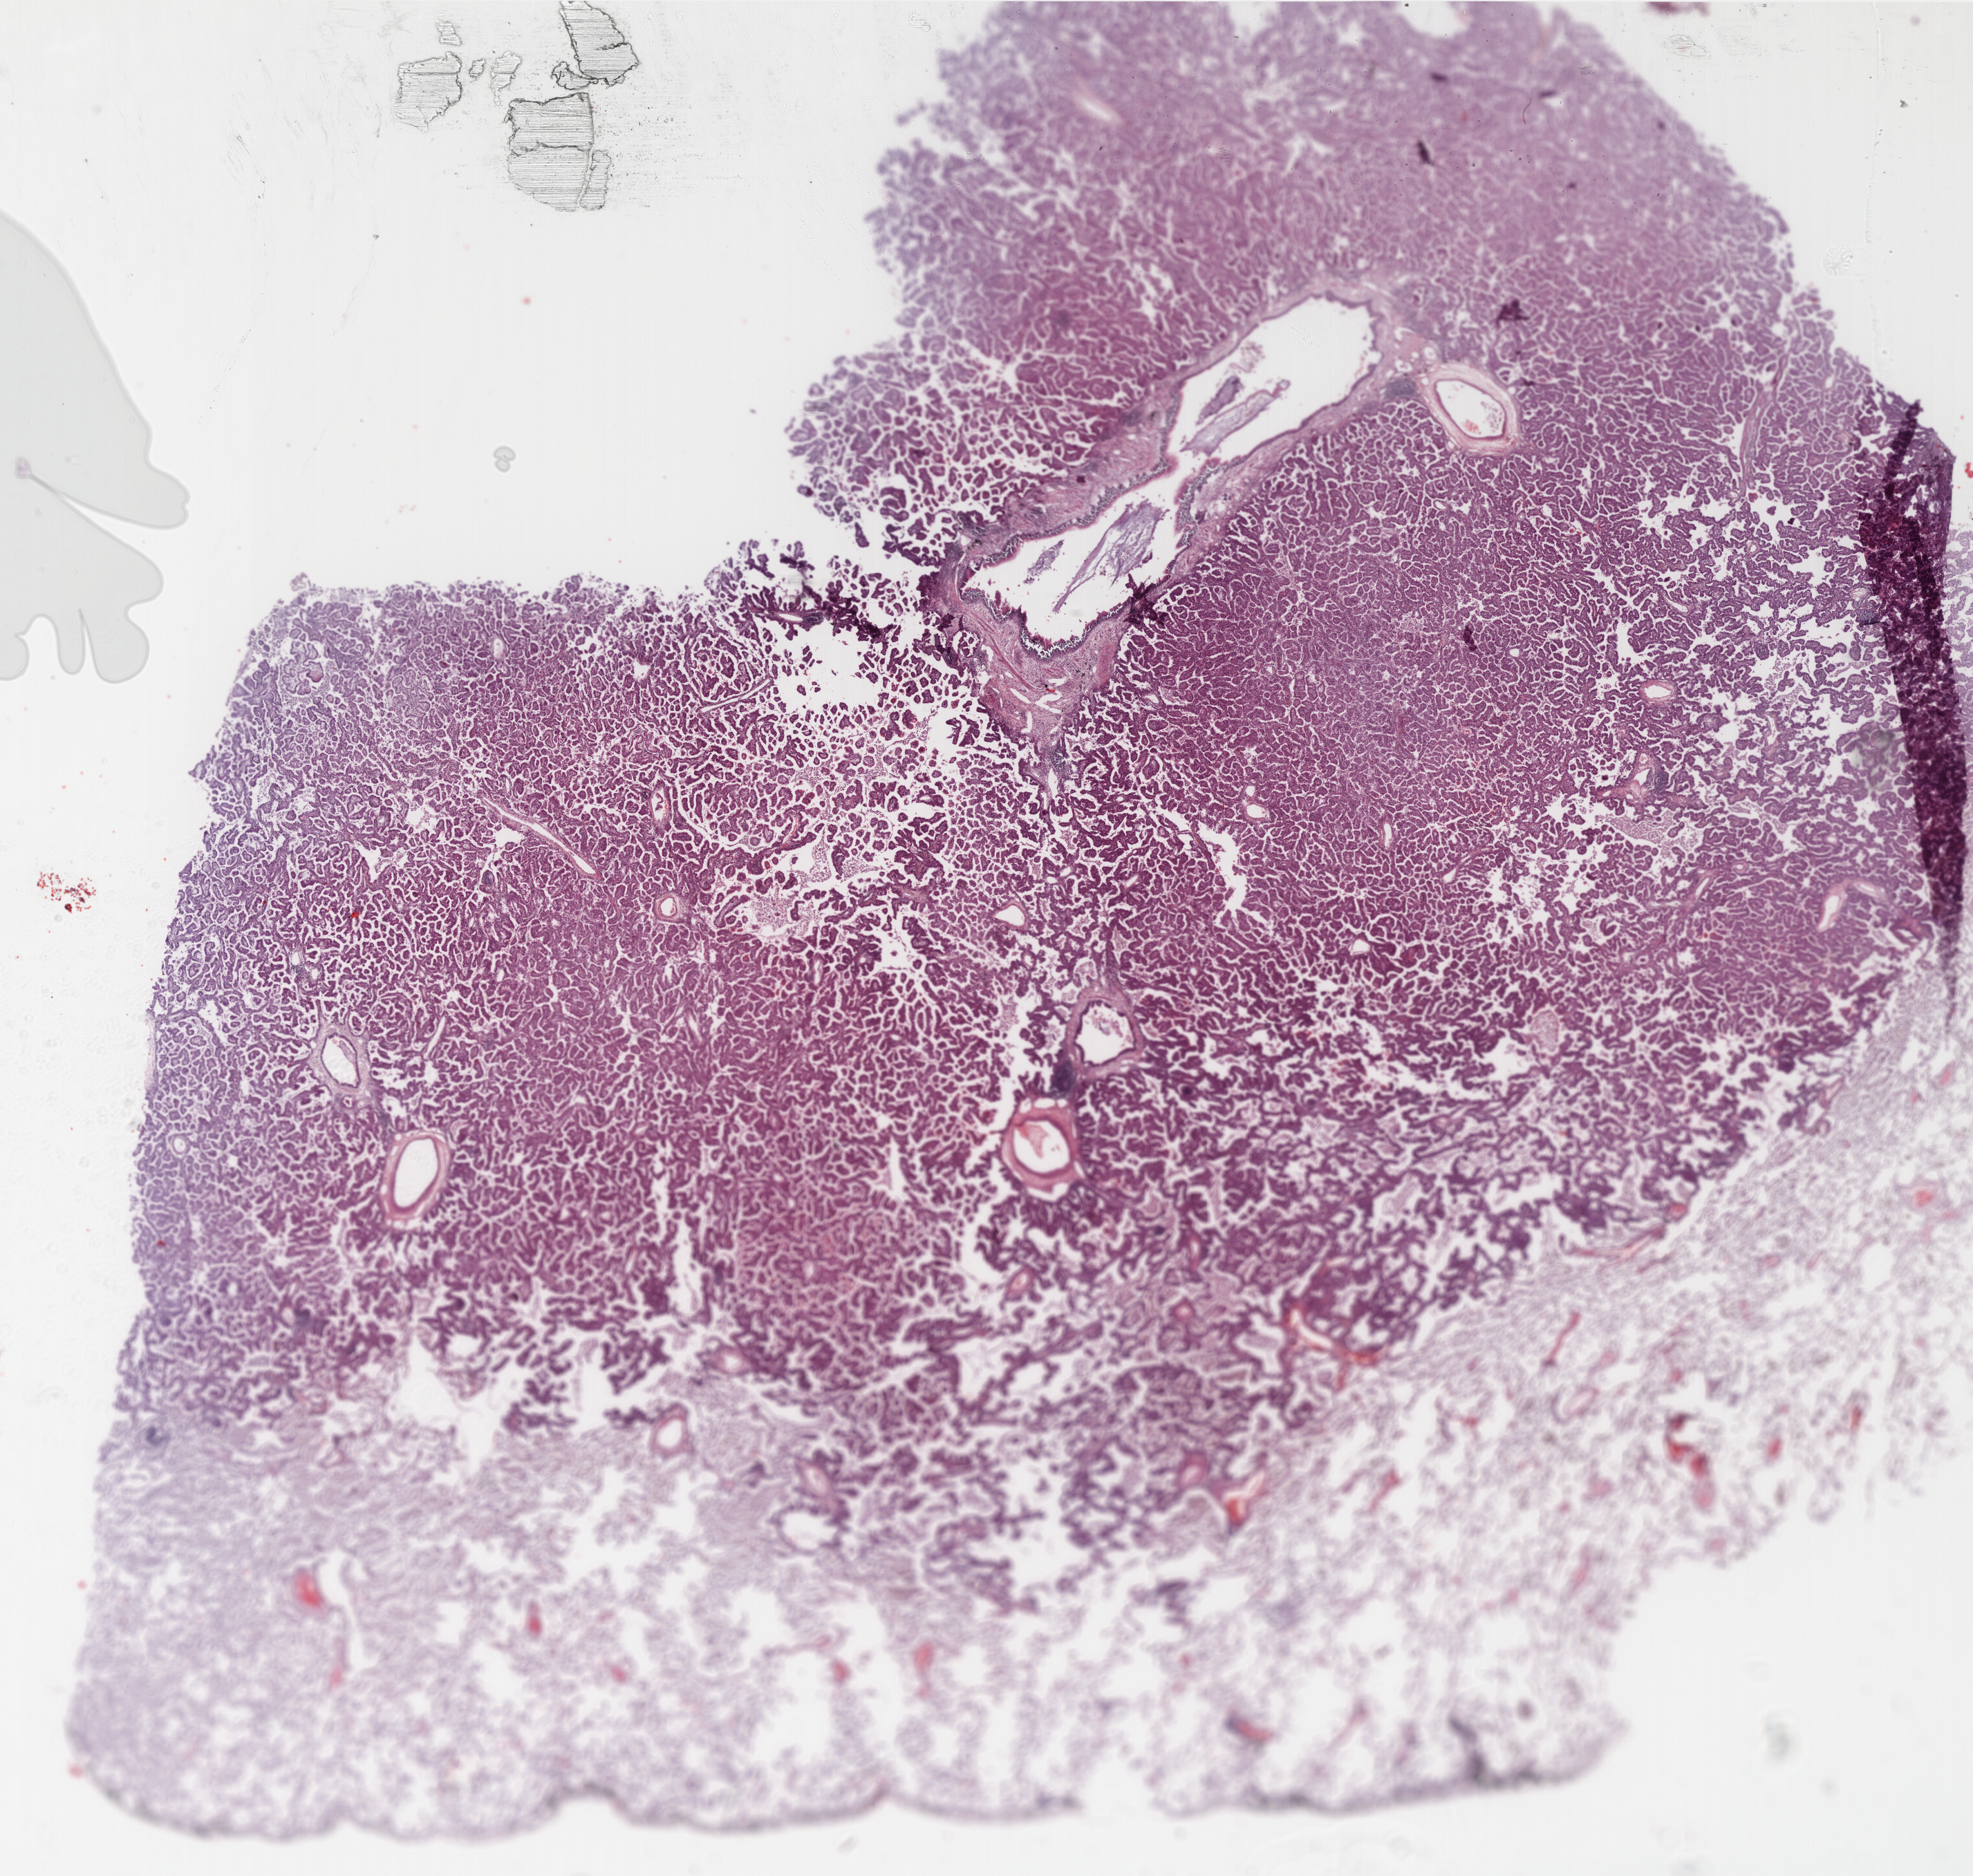
Digitized H&E-stained tissue section (whole slide), a low-resolution overview of the entire scanned area, about 23.0 x 21.9 mm. Formalin-fixed paraffin-embedded (FFPE) diagnostic section. Primary tumour sample from the lung. Male patient; age at initial diagnosis 65 years.
Pathologic diagnosis: Adenocarcinoma with mixed subtypes.